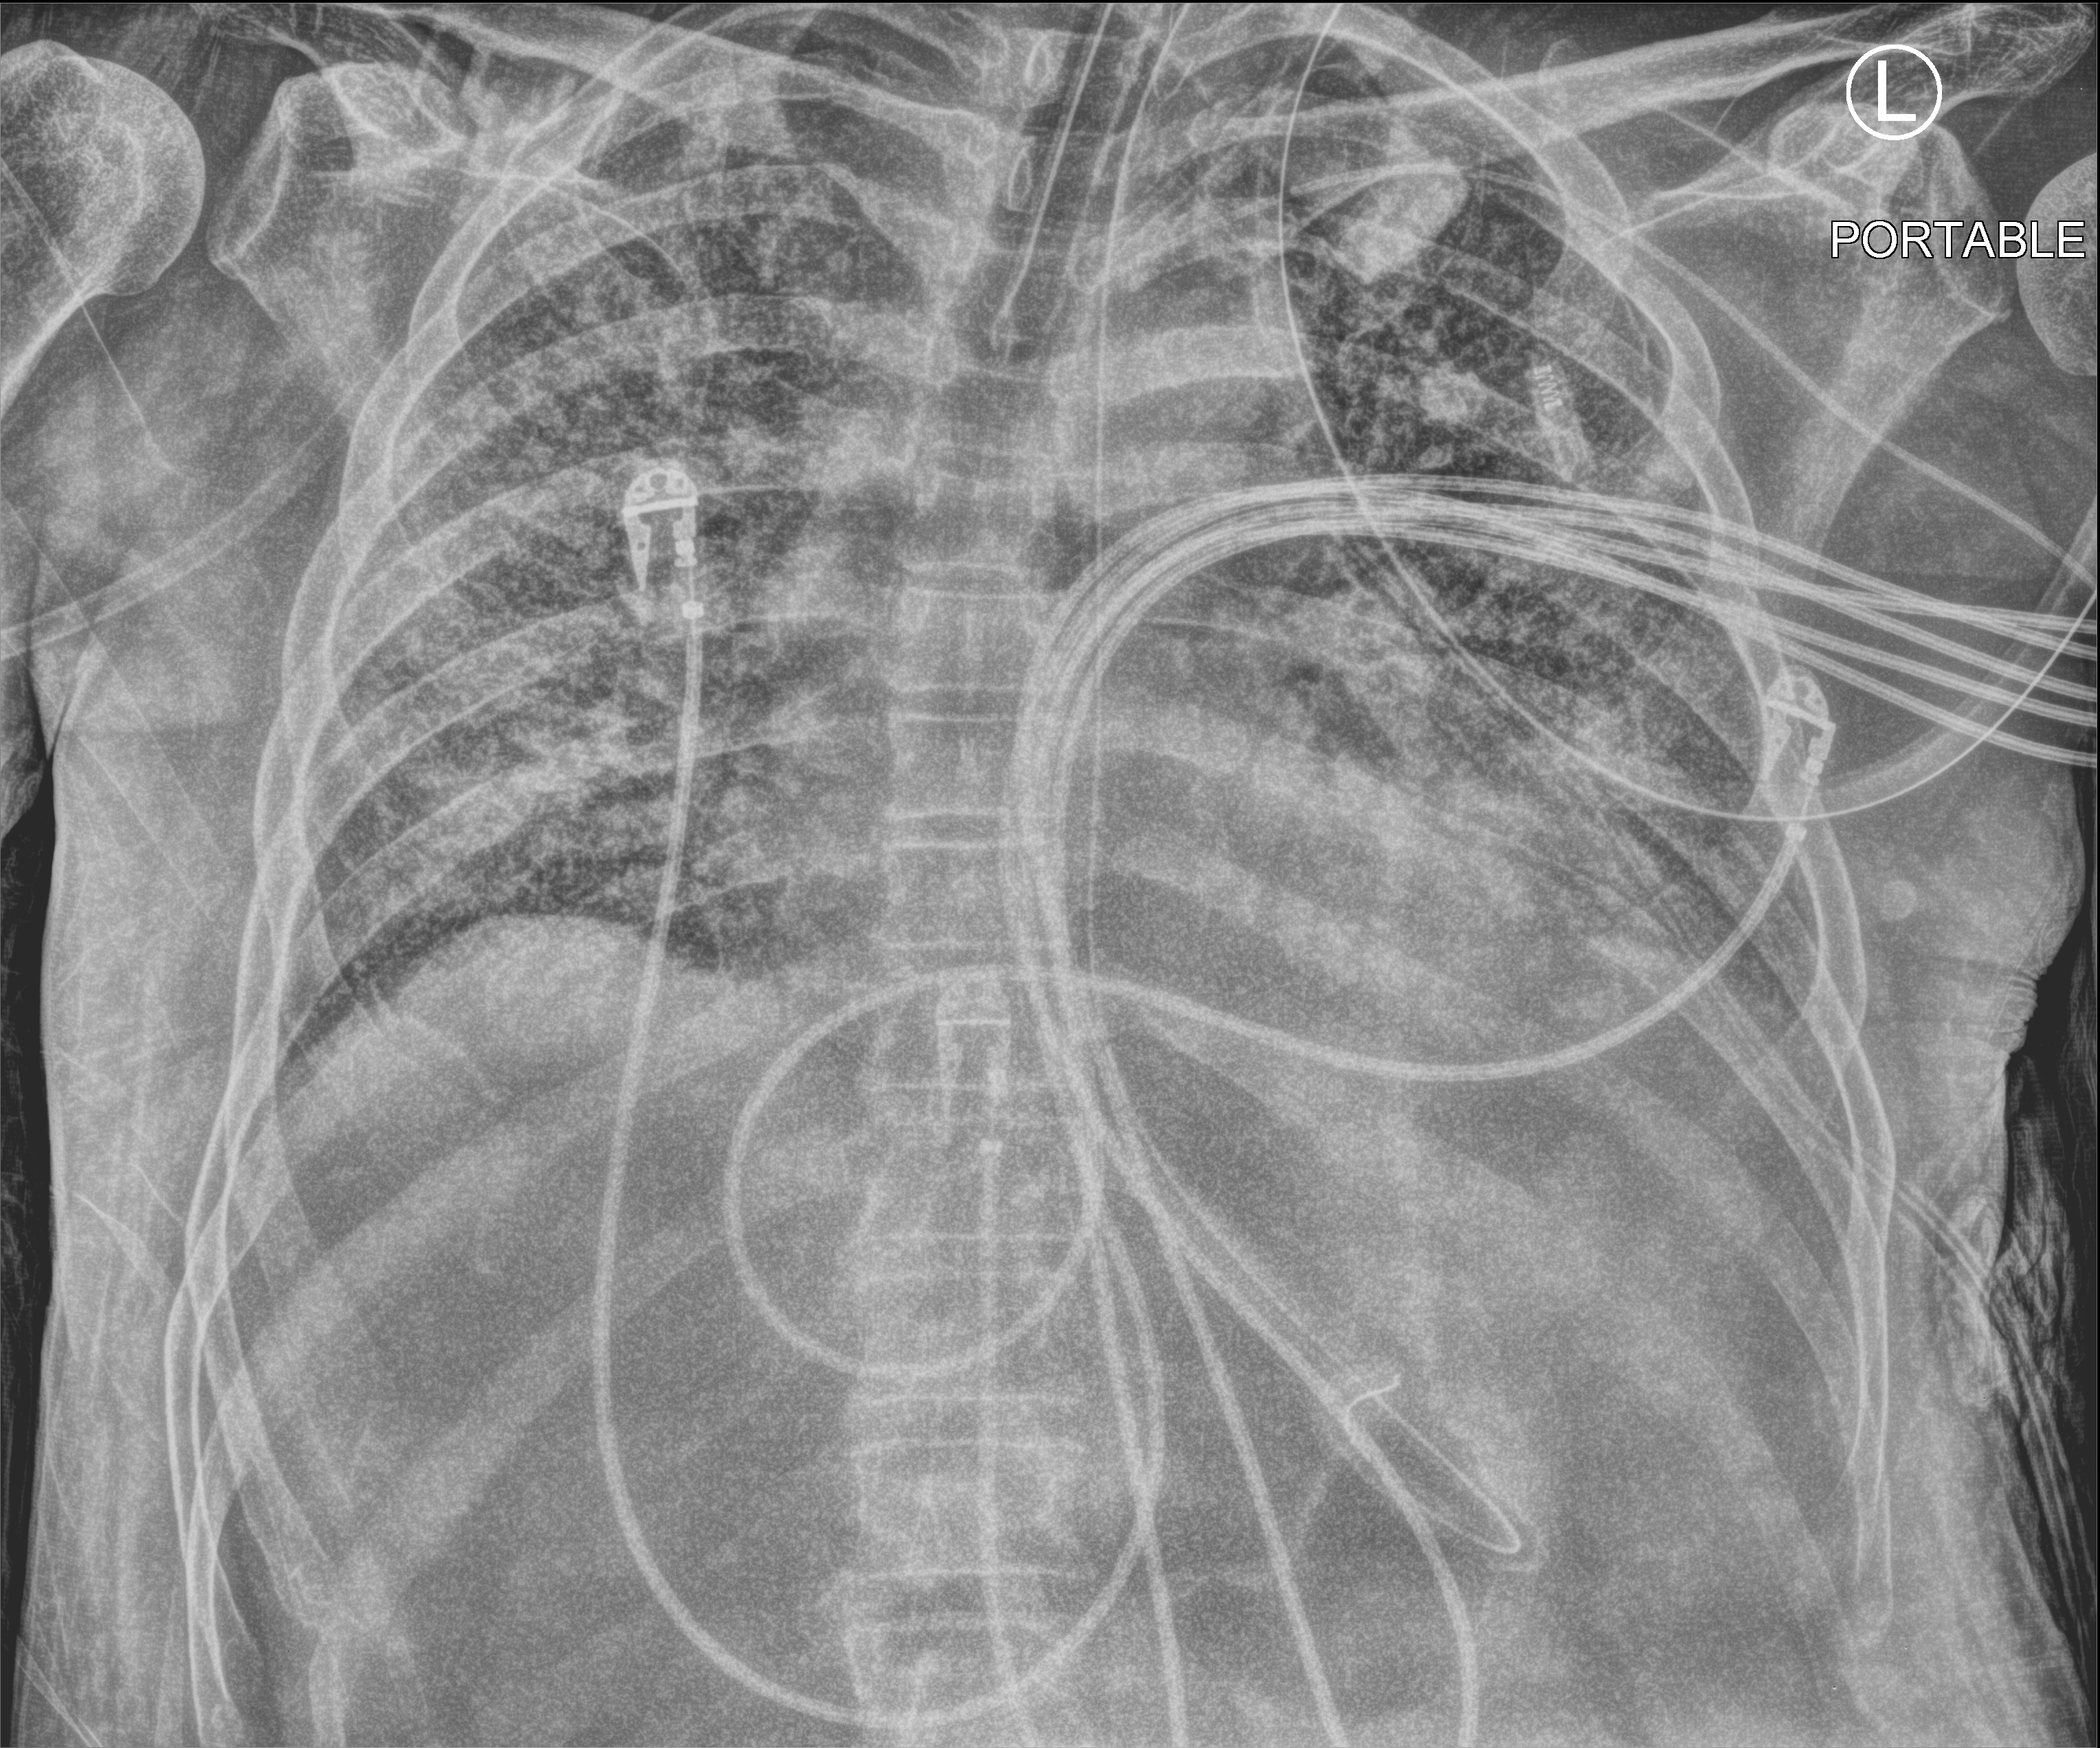
Portable chest radiograph, anteroposterior (AP) projection. Patient hospitalised with COVID-19; male, aged 60–74 years.
From the hospital-stay record, not from the radiograph (when in the stay this image was taken is not recorded):
- mechanically ventilated during this hospital stay: yes